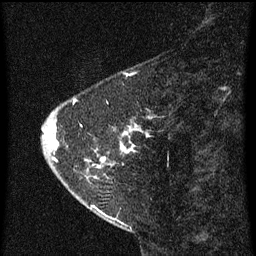
Breast MRI (dynamic contrast-enhanced), one sagittal slice. Position 16 of 60 along the scan axis. Dynamic contrast-enhanced series, image 2 of 3 at this slice position (ordered by acquisition). 1.5 T. TE 4.2 ms, TR 8 ms. 2 mm slice thickness. 256 × 256 image matrix, field of view 180 × 180 mm. Female patient, age 47 years.
Structures marked on this image (semi-automatic segmentation, software-assisted and operator-edited):
- analysis volume of interest (the breast-tissue region the enhancement analysis was run in; not a lesion): bounding box (x1, y1, x2, y2) in pixels: (44, 96, 155, 199)
- tumour enhancement mask (voxels above the 70 % enhancement threshold inside the analysis volume of interest): (44, 100, 149, 167)